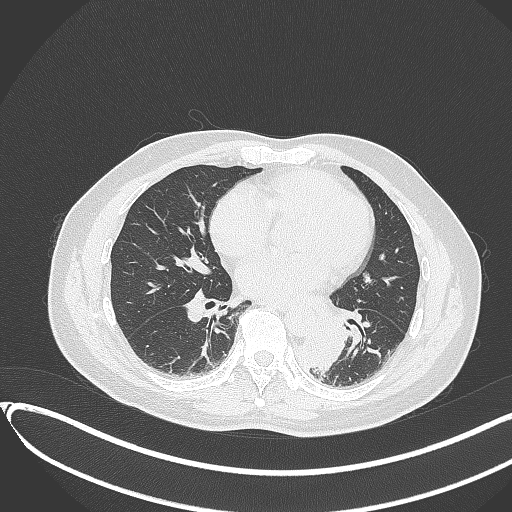
Chest CT, one axial slice. Lung window (W 1500 / L -600 HU). 512 × 512 image matrix, field of view 400 × 400 mm. Male patient, age 54 years. Case-level facts recorded for this patient, not image findings: clinical TNM (as recorded): T3 N0 M0.
Annotated regions visible in this slice (bounding box drawn by a radiologist):
- lung tumour (recorded histology: squamous cell carcinoma): box from (x=299, y=325) to (x=346, y=377) px